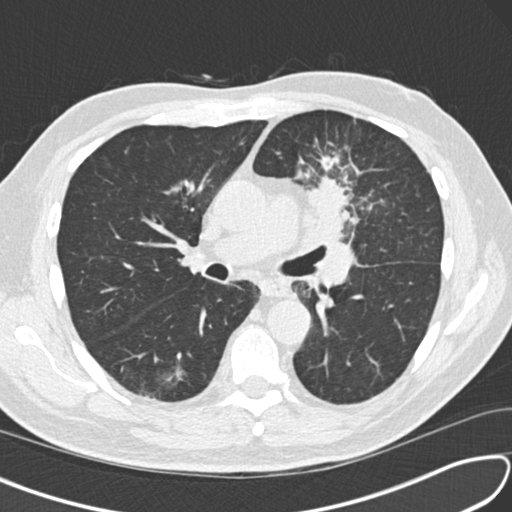
Low-dose screening chest CT, one axial slice; lung window (W 1500 / L -600 HU); 2 mm slice thickness; 512 × 512 image matrix.
Structures marked on this image (manually delineated by an expert):
- lesion 1 (tumor, upper lobe of left lung): bounding box <306,175,349,237> (left, top, right, bottom; pixels)